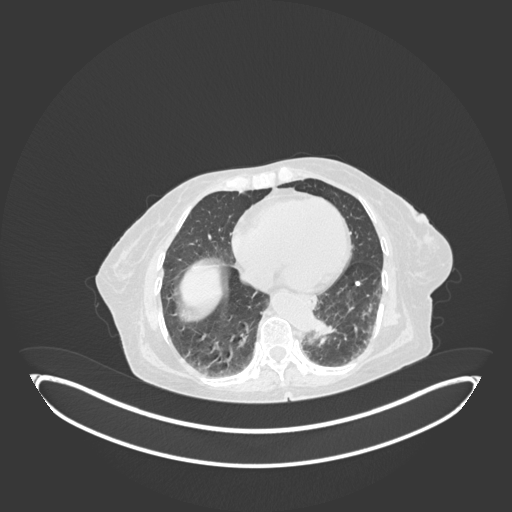
Chest CT, one axial slice; position 23 of 189 along the scan axis; lung window (W 1500 / L -600 HU); 1 mm slice thickness; 512 × 512 image matrix, field of view 500 × 500 mm. Female patient, age 82 years. From the clinical record (not read from this slice): clinical TNM (as recorded): T1b N0 M1.
Annotated regions visible in this slice (bounding box drawn by a radiologist):
- lung tumour (recorded histology: adenocarcinoma): bounding box <312,319,337,344> (left, top, right, bottom; pixels)